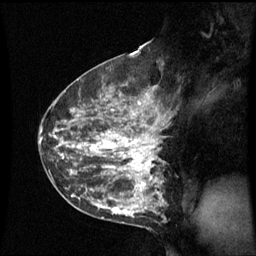
Breast MRI (dynamic contrast-enhanced), one sagittal slice. Position 33 of 60 along the scan axis. Dynamic contrast-enhanced series, image 2 of 3 at this slice position (ordered by acquisition). 1.5 T. TE 4.2 ms, TR 8.9 ms. 2.4 mm slice thickness. 256 × 256 image matrix. Patient: female, 42 years. Case-level facts recorded for this patient, not image findings: setting: breast cancer imaged before/during neoadjuvant chemotherapy; receptor status: HER2-positive.
Structures marked on this image (semi-automatically segmented with operator editing):
- analysis volume of interest (the breast-tissue region the enhancement analysis was run in; not a lesion): bounding box (x1, y1, x2, y2) in pixels: (62, 93, 166, 210)
- tumour enhancement mask (voxels above the 70 % enhancement threshold inside the analysis volume of interest): (80, 95, 160, 192)